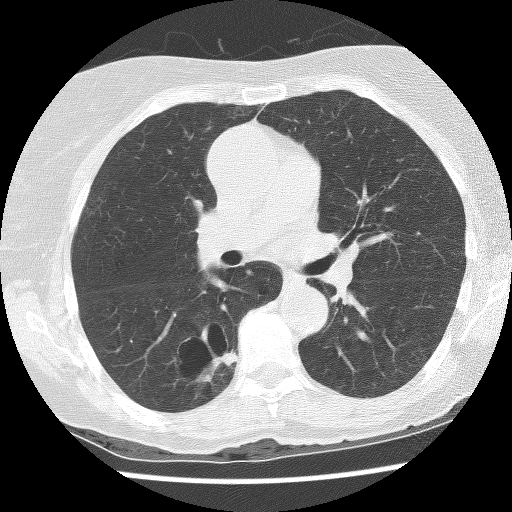
Low-dose screening chest CT, axial slice, first (baseline) screen, lung window (W 1500 / L -600 HU), 2.5 mm slice thickness, lung (sharp) reconstruction kernel (BONE), slice 55 of 136 in the series. Female, age 69 years at enrolment. Former smoker at enrolment.
Lesion marked by an expert reader, bounding box <155,319,247,395> (left, top, right, bottom; pixels). The screening reader recorded 2 non-calcified nodules or masses ≥4 mm on this exam (right lower lobe, right lower lobe); which of them this box marks is not recorded. Lung cancer was diagnosed 288 days after this screen: non-small cell carcinoma, right lower lobe, poorly differentiated (G3), stage IB (AJCC 6th edition), 36 mm at pathology.